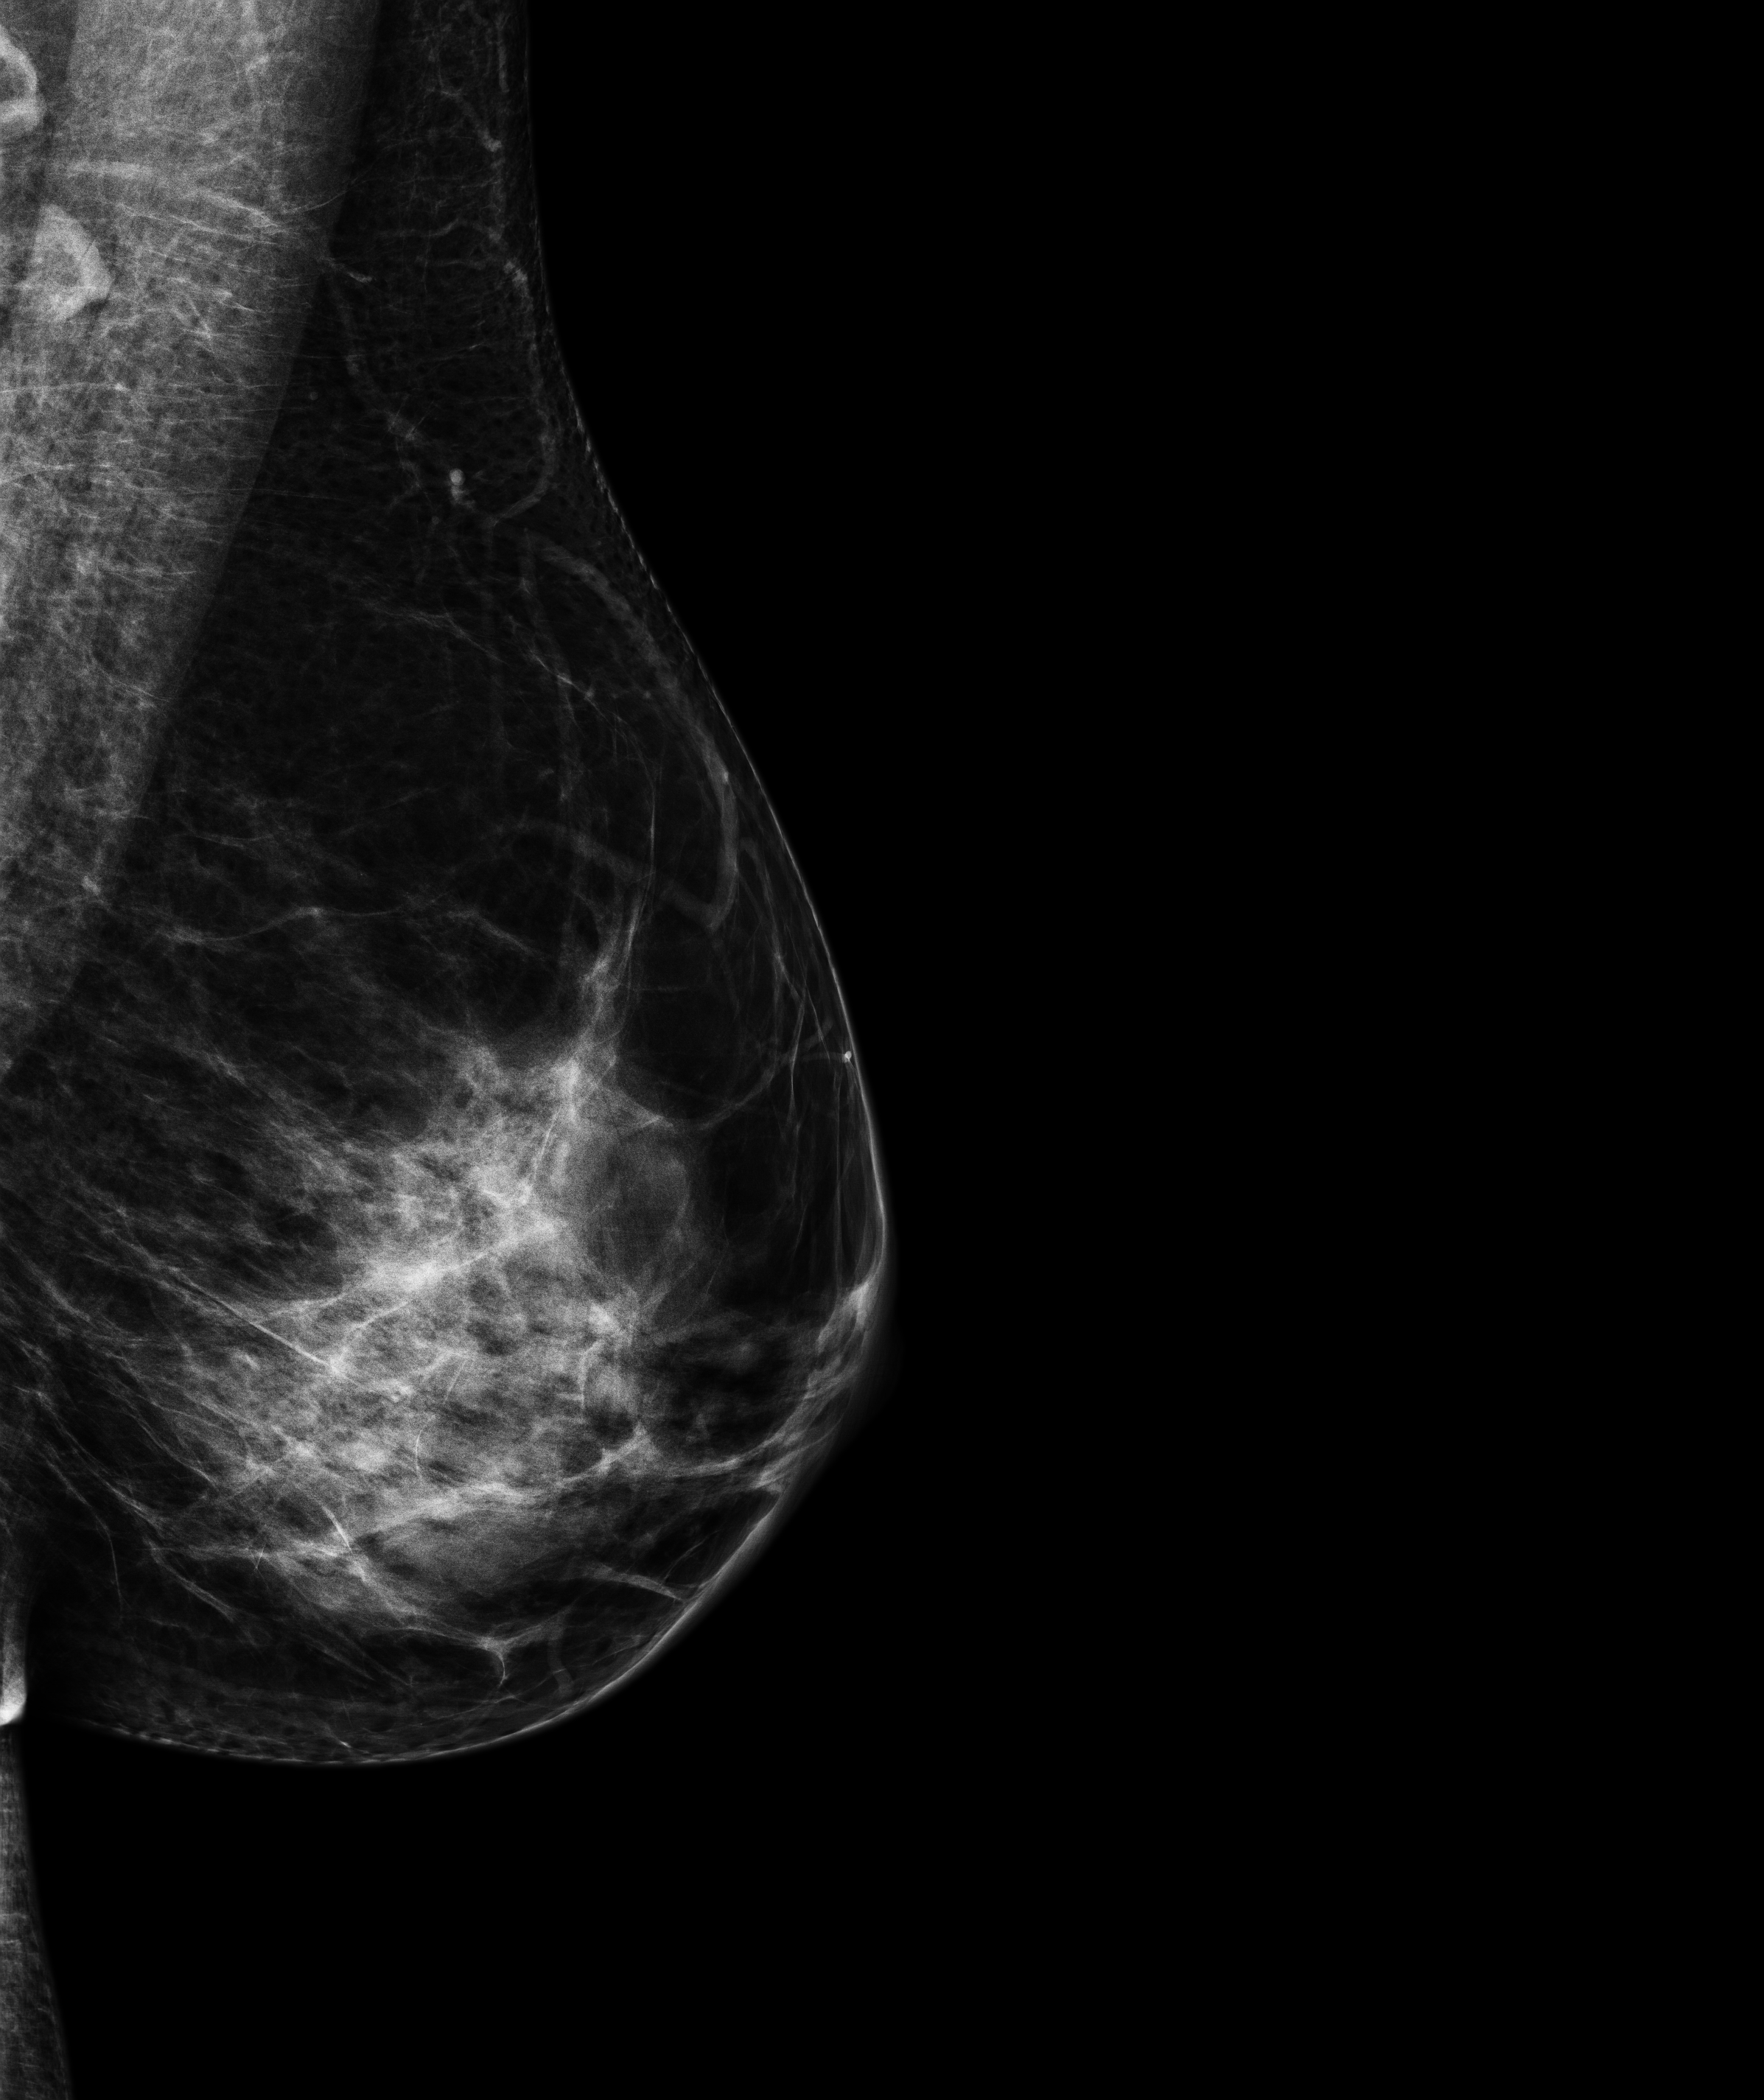
Screening examination; system: Senographe Pristina. Patient aged 45 years (female).
Image type: full-field digital mammogram. Breast: left. Projection: medio-lateral oblique projection.